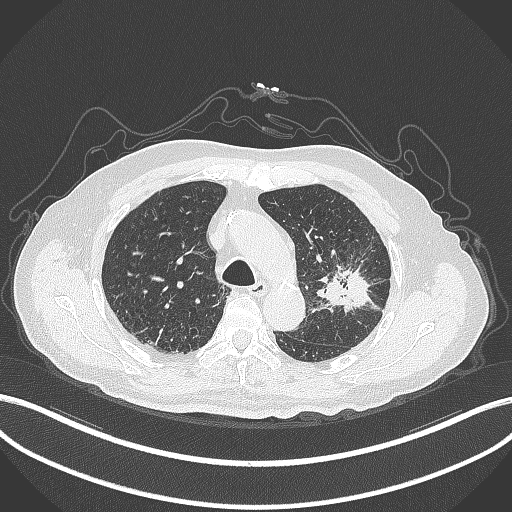
Chest CT, one axial slice; position 211 of 331 along the scan axis; reconstruction kernel B70f; lung window (W 1500 / L -600 HU); 1 mm slice thickness; 512 × 512 image matrix, field of view 400 × 400 mm. Patient: male, 79 years. Case-level facts recorded for this patient, not image findings: clinical TNM (as recorded): T2a N1 M1.
Structures marked on this image (bounding box drawn by a radiologist):
- lung tumour (recorded histology: adenocarcinoma): bounding box <313,258,378,316> (left, top, right, bottom; pixels)